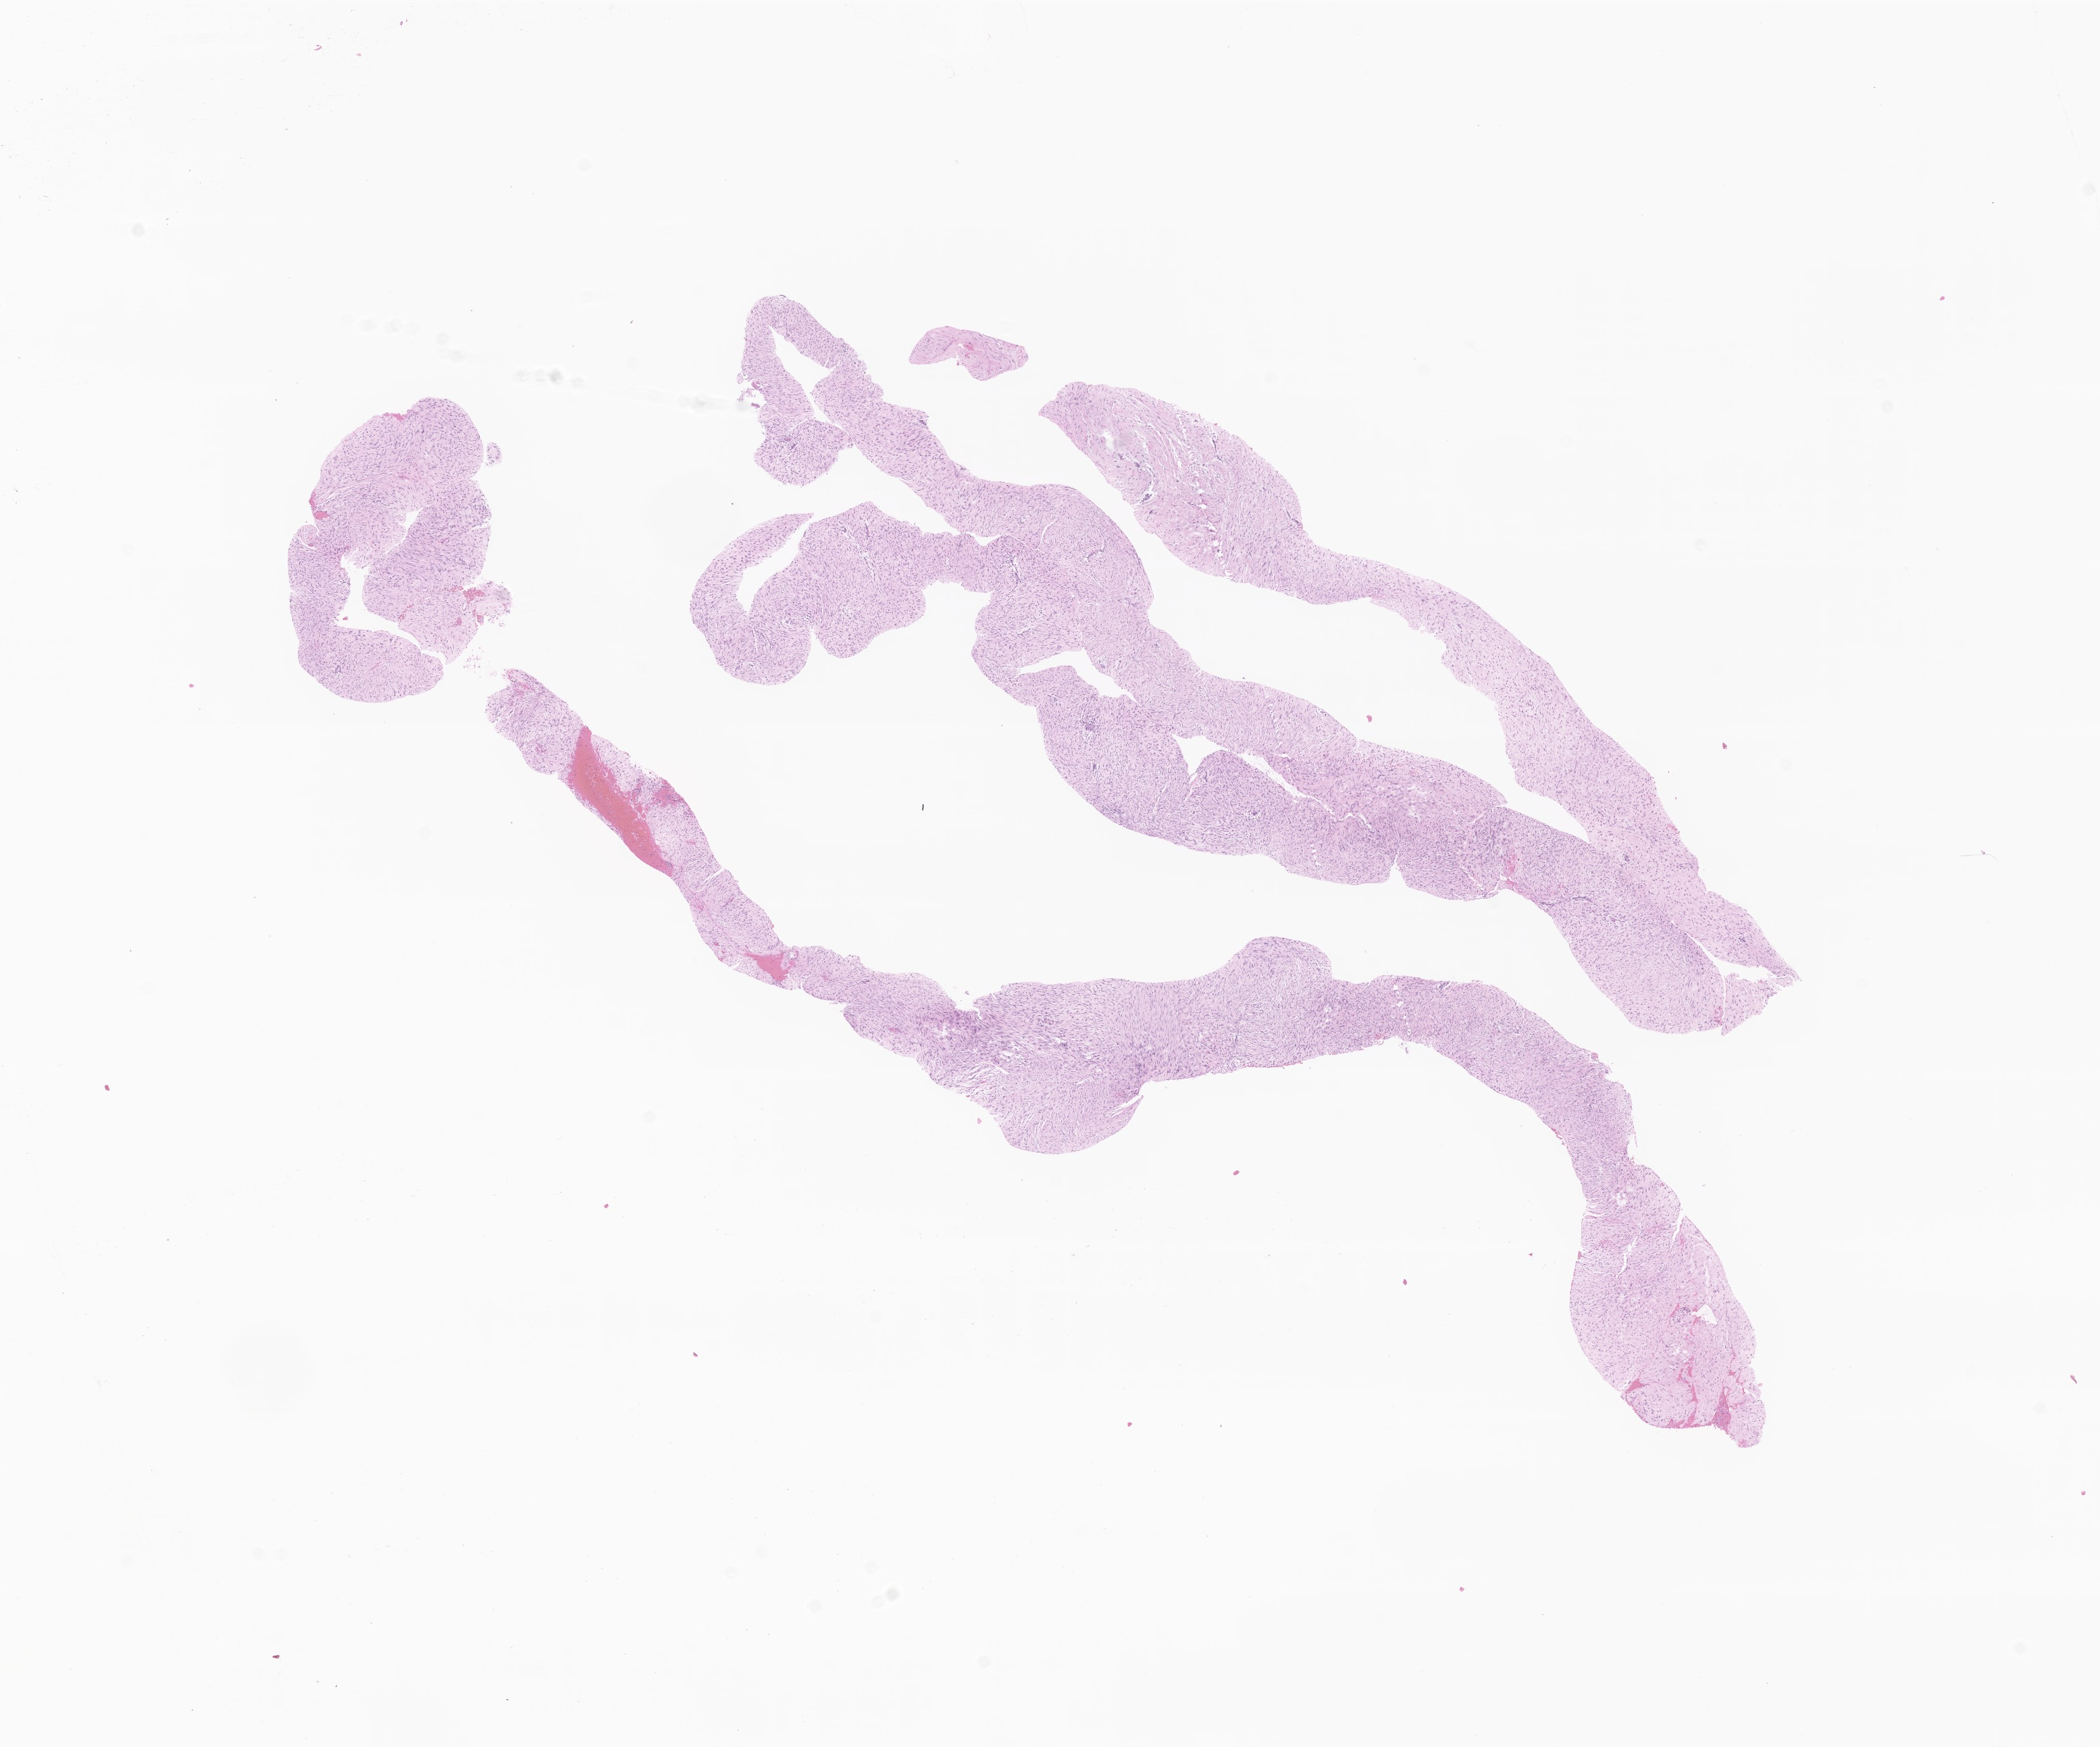
H&E whole-slide image of tumor tissue from the soft tissues of head and neck — whole scanned area (about 13.1 x 10.9 mm) shown as a low-resolution overview, formalin-fixed, paraffin-embedded (FFPE) tissue. Patient female; age 205 months (17 years 1 month).
Recorded diagnosis: Aggressive fibromatosis.